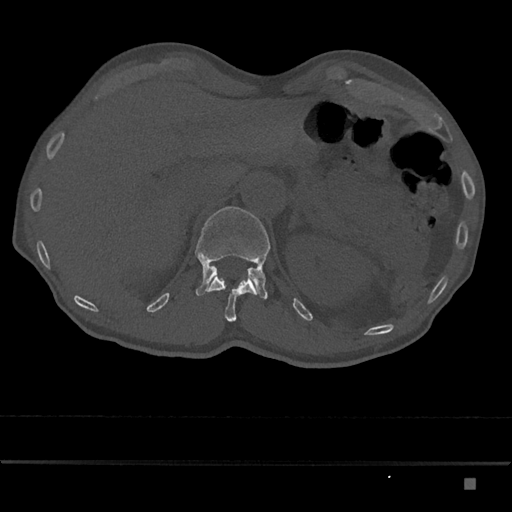
CT including the spine, one axial slice; slice 578 of 797 in the series (ordered by position); reconstruction kernel Br40s/3; 120 kVp; bone window (W 1800 / L 400 HU); 0.5 mm slice thickness; 512 × 512 image matrix, field of view 390 × 390 mm. Patient: male, 72 years. Case-level facts recorded for this patient, not image findings: primary cancer: prostate.
Structures marked on this image (semi-automatic segmentation, software-assisted and operator-edited):
- L1 vertebra: bounding box <195,206,270,300> (left, top, right, bottom; pixels)
- T12 vertebra: <205,275,256,322>